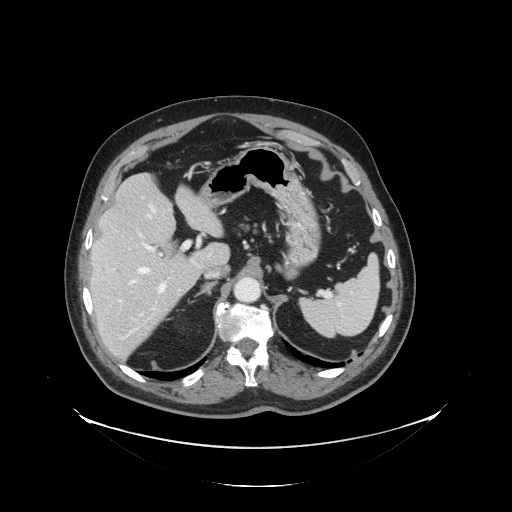
Contrast-enhanced abdominal CT, one axial slice. Position 91 of 138 along the scan axis. 120 kVp. Intravenous contrast given. Soft-tissue window (W 400 / L 40 HU). 2.5 mm slice thickness. 512 × 512 image matrix, field of view 497 × 497 mm. Male patient, age 77 years. Case-level facts recorded for this patient, not image findings: diagnosis: colorectal cancer liver metastases, imaged before liver resection; multiple liver metastases: no; largest metastasis: 1.5 cm; disease in both lobes: no.
Outlined on this slice (outlined manually by an expert reader):
- hepatic veins: bounding box <127,205,156,336> (left, top, right, bottom; pixels)
- liver: <91,174,229,359>
- planned liver remnant (the part of the liver to remain after resection): <92,174,227,288>
- portal vein (with intrahepatic branches): <117,242,189,303>